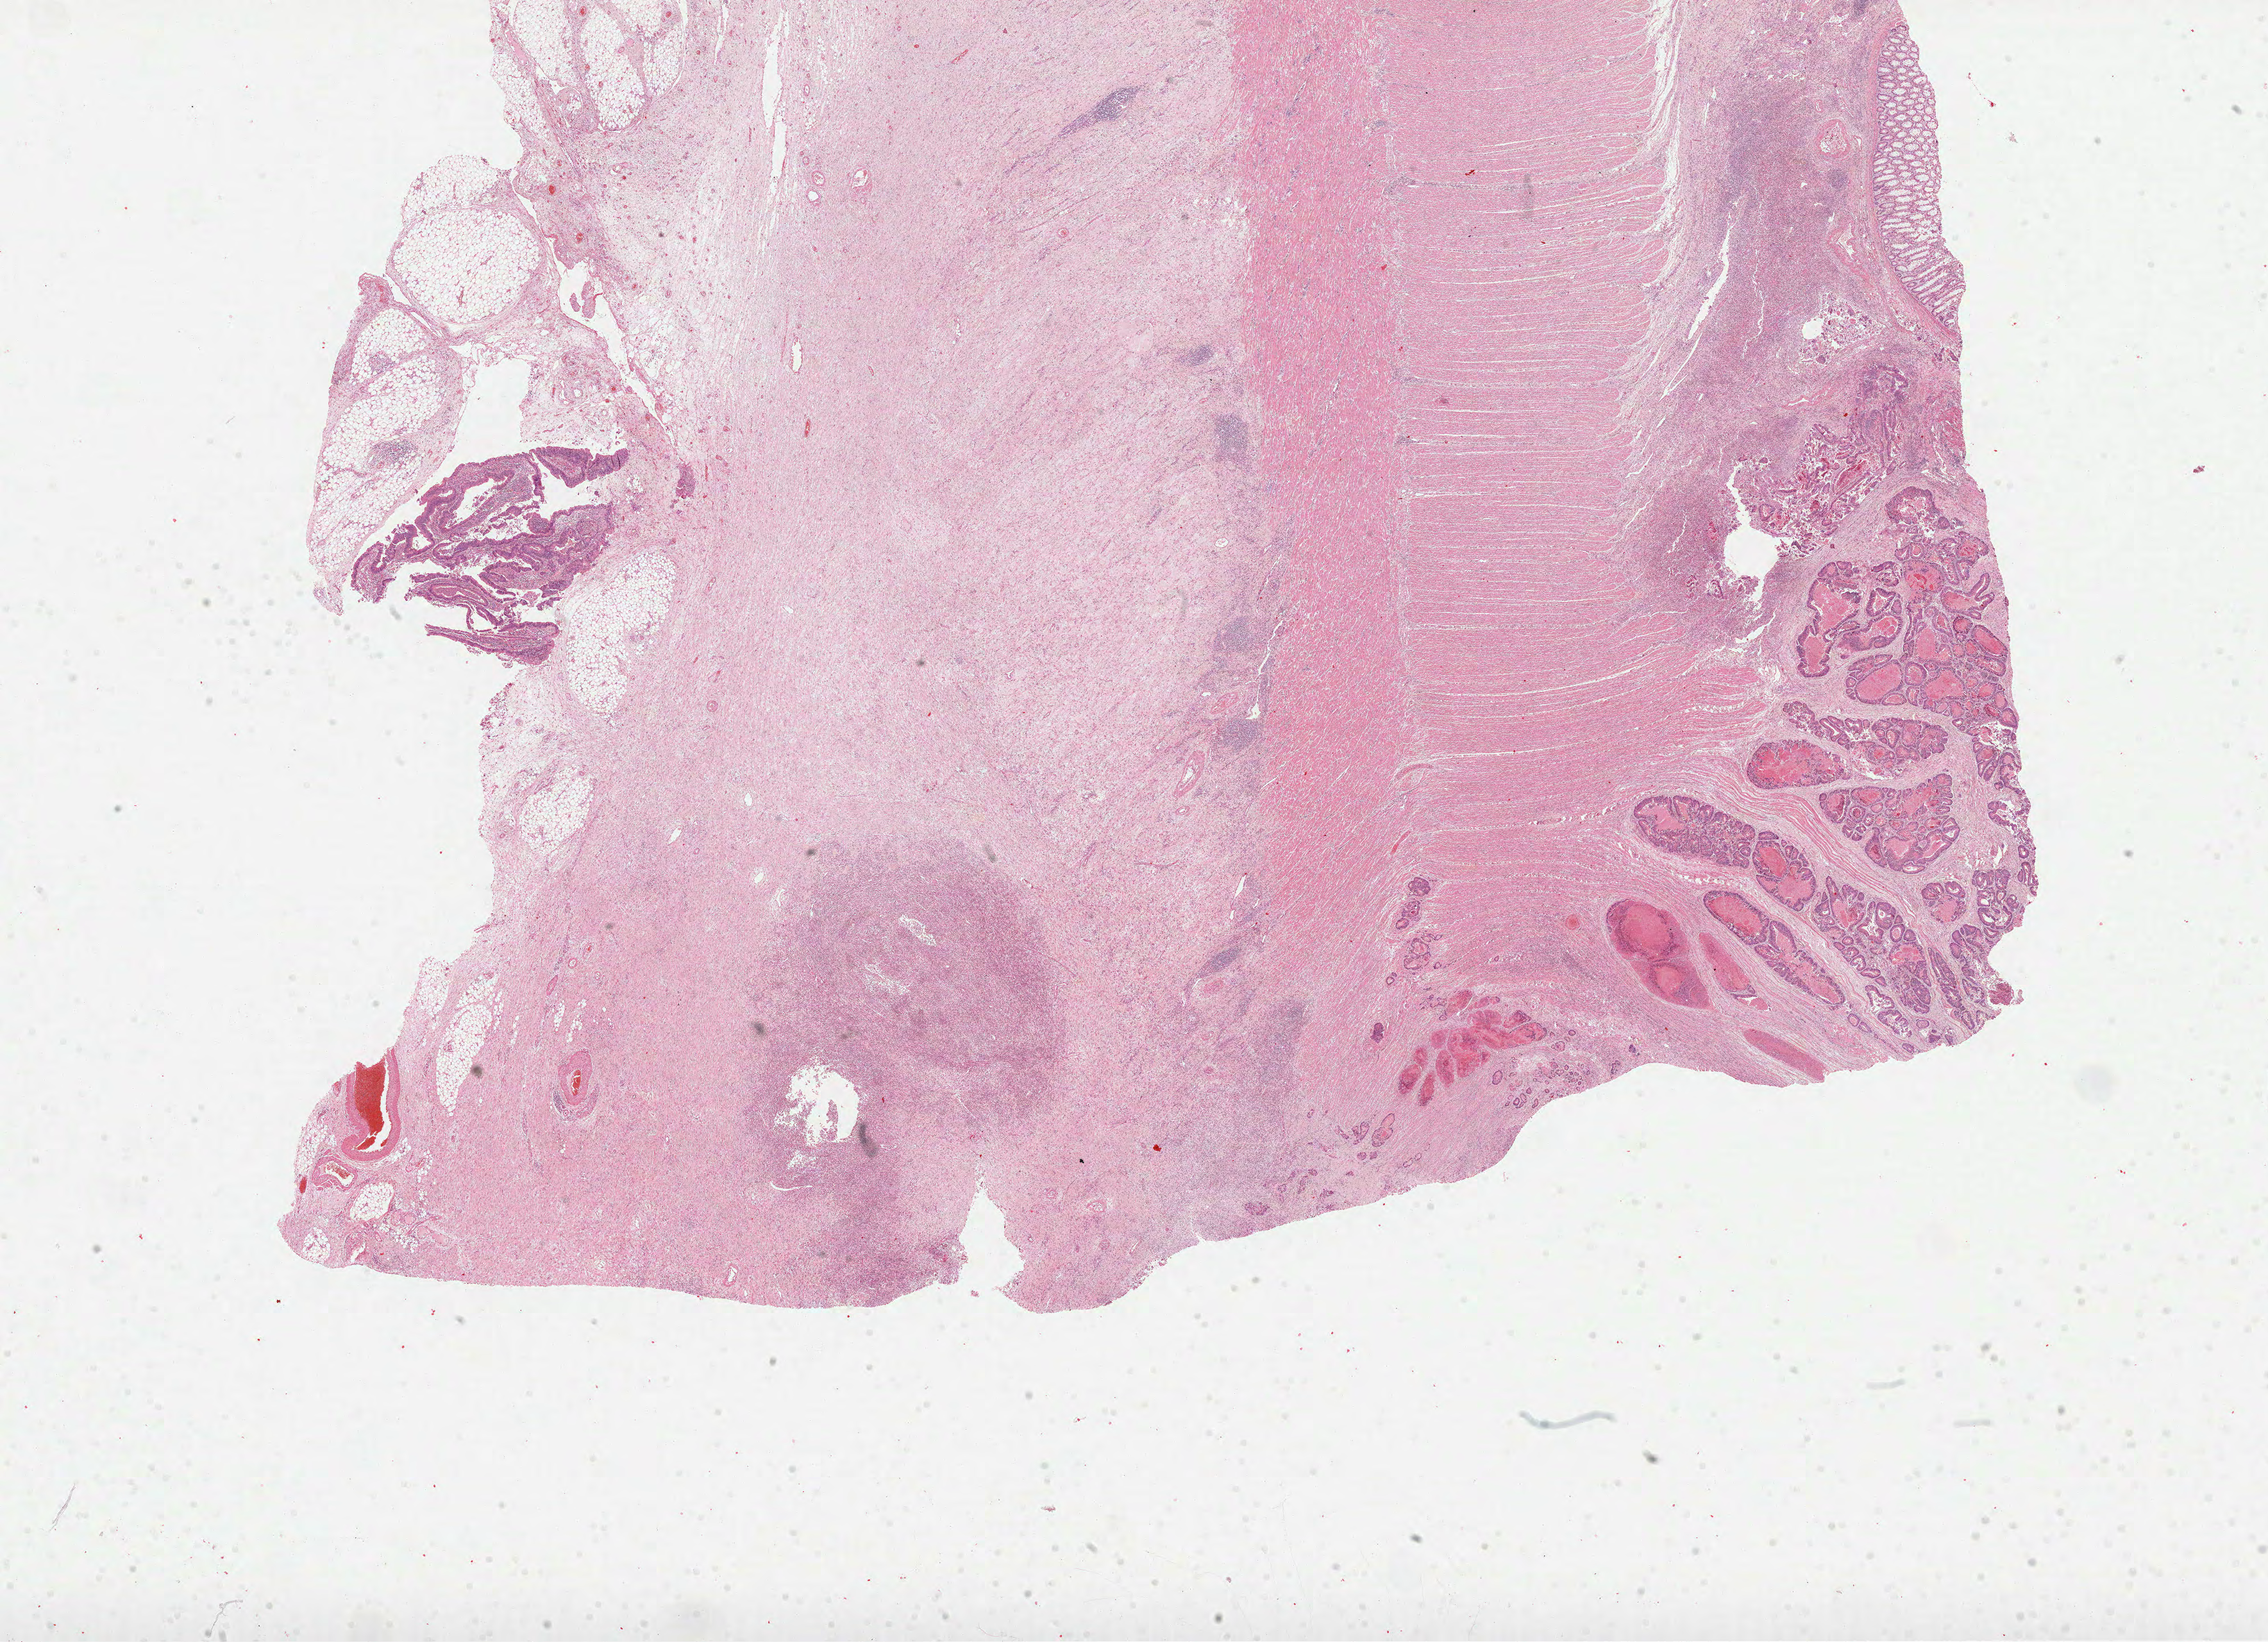
Digitized H&E-stained tissue section (whole slide), shown as a low-resolution overview of the whole scanned area (about 28.5 x 20.7 mm), formalin-fixed paraffin-embedded (FFPE) diagnostic section, sample: primary tumour, colon. Female, age 68 years at initial diagnosis.
* diagnosis: Adenocarcinoma, NOS (transverse colon)
* lymph nodes positive (case pathology): 0 of 8 examined